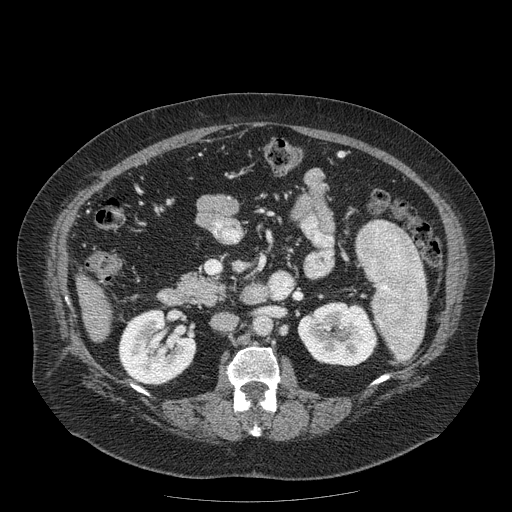
Contrast-enhanced abdominal CT (liver protocol), one axial slice; position 55 of 204 along the scan axis; 120 kVp; soft-tissue window (W 400 / L 40 HU); 512 × 512 image matrix. From the clinical record (not read from this slice): diagnosis: hepatocellular carcinoma (patient treated with transarterial chemoembolisation; whether this scan precedes or follows treatment is not stated here); TNM stage (as recorded): Stage-IIIB; Child-Pugh class: A; tumour differentiation: well differentiated; tumour nodularity: uninodular.
Structures marked on this image (semi-automatically segmented with operator editing):
- liver parenchyma outside the tumour (the mass and vessels are separate outlines, so this box may not span the whole liver): box from (x=76, y=274) to (x=110, y=340) px